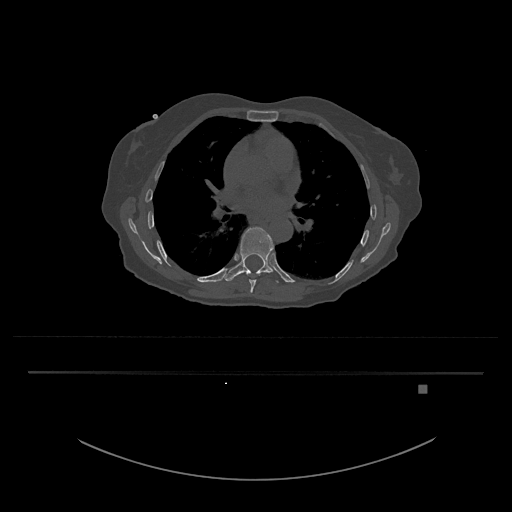
CT including the spine, one axial slice; bone window (W 1800 / L 400 HU); 0.5 mm slice thickness; 512 × 512 image matrix, field of view 500 × 500 mm. Female patient, age 57 years. From the clinical record (not read from this slice): primary cancer: cervical.
Annotated regions visible in this slice (semi-automatically segmented with operator editing):
- T8 vertebra: bounding box [x1, y1, x2, y2] px = [246, 272, 262, 293]
- T9 vertebra: [224, 227, 279, 283]